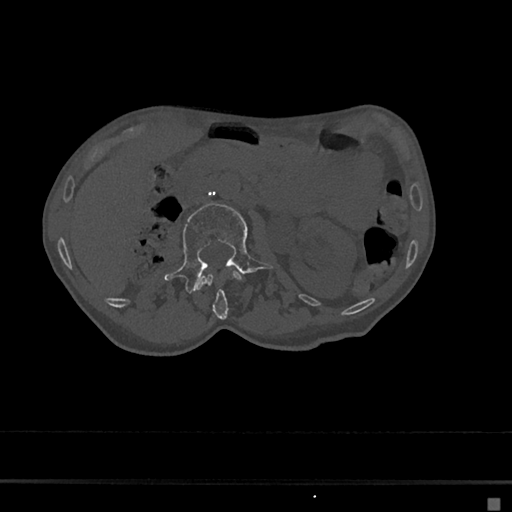
CT including the spine, one axial slice. Slice 26 of 797 in the series (ordered by position). 120 kVp. Bone window (W 1800 / L 400 HU). 0.5 mm slice thickness. 512 × 512 image matrix, field of view 360 × 360 mm. Patient: female, 68 years. From the clinical record (not read from this slice): primary cancer: renal.
Structures marked on this image (semi-automatic segmentation, software-assisted and operator-edited):
- L1 vertebra: bounding box <197,270,242,319> (left, top, right, bottom; pixels)
- L2 vertebra: <164,203,274,293>